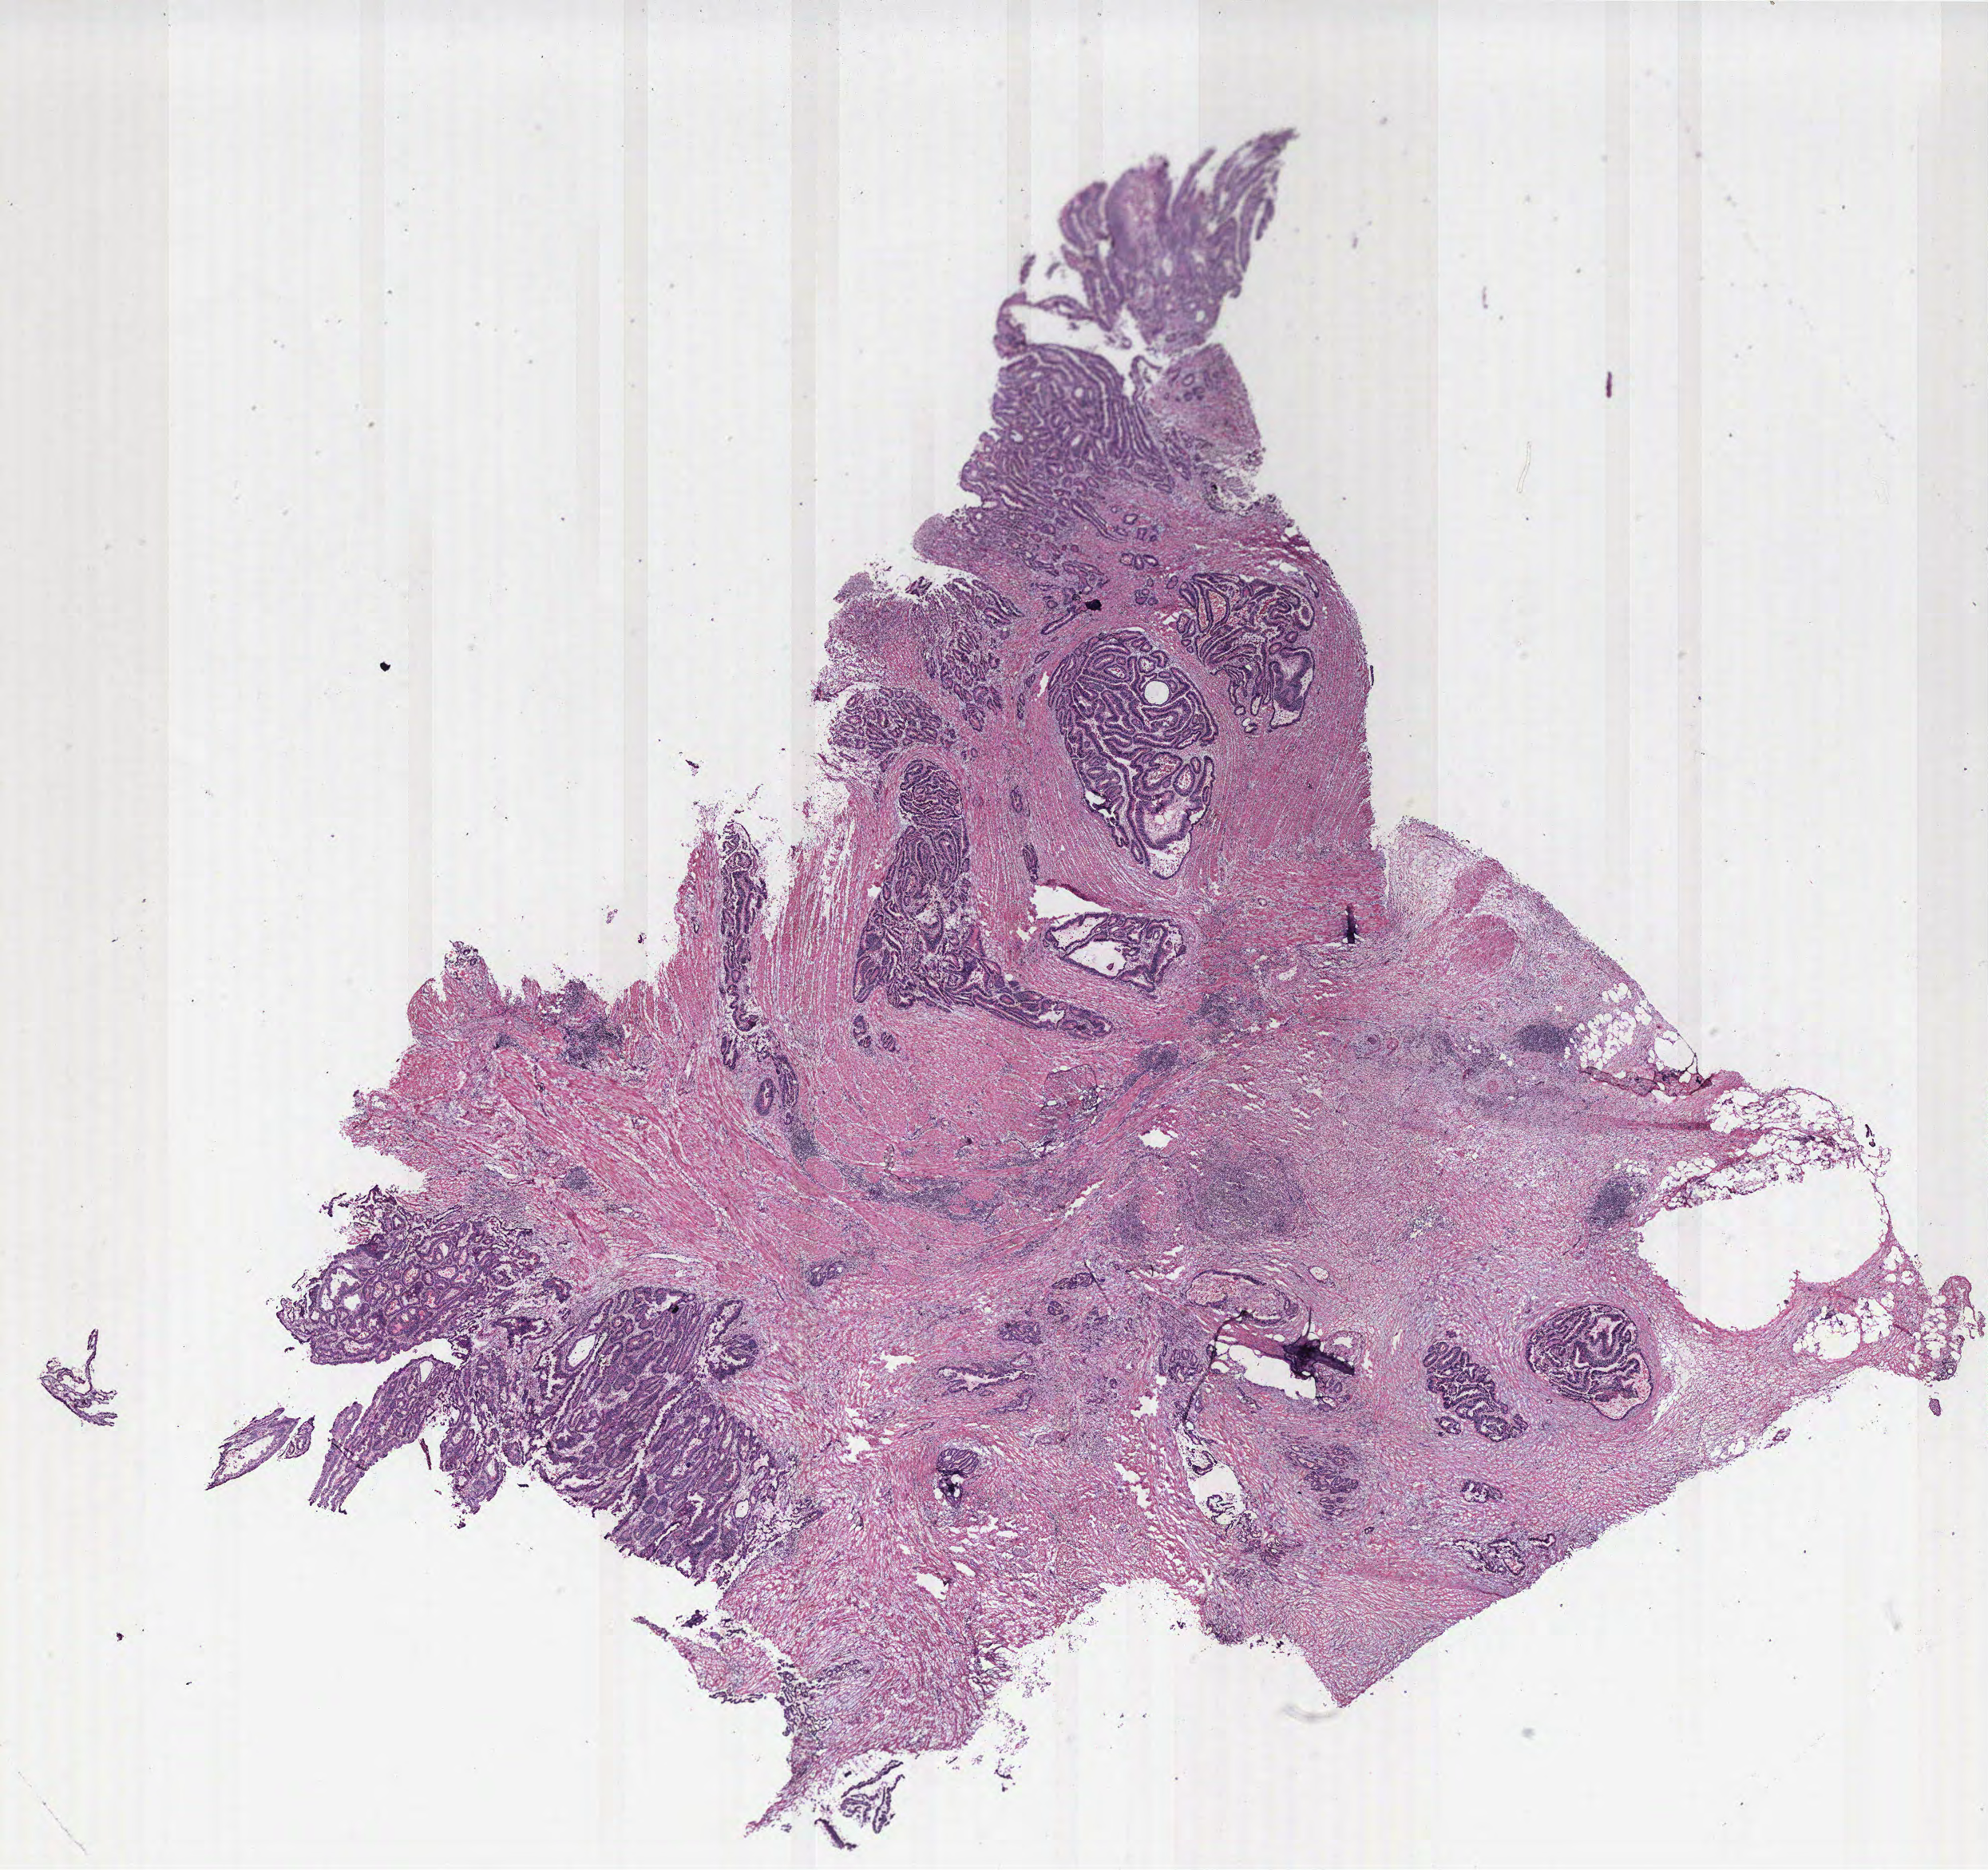
Digitized H&E tissue section (whole slide) — a low-resolution overview of the entire scanned area, about 19.9 x 18.7 mm. Colon, tissue type not recorded. Male patient.
Patient diagnosis: Adenocarcinoma, NOS.